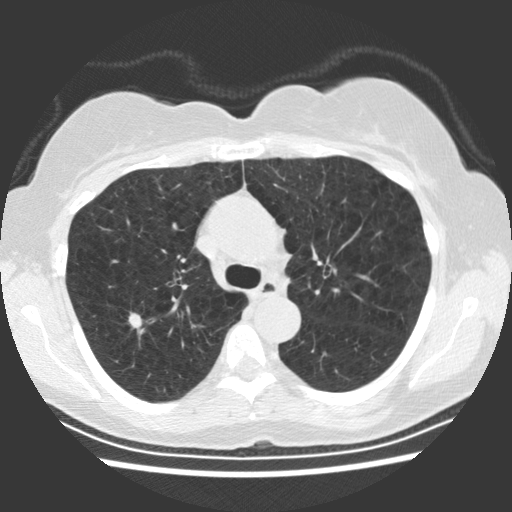
Chest CT (low-dose screening protocol), one axial image; baseline annual screen; lung window (W 1500 / L -600 HU); 2.5 mm slice thickness. Female, age 66 years at enrolment.
• Expert reader's lesion annotation, bounding box (x1, y1, x2, y2) in pixels: (111, 301, 153, 339).
• Screening reader's record for this exam (one nodule recorded; not confirmed to be the boxed lesion): non-calcified nodule or mass ≥4 mm, right upper lobe, 10 × 8 mm, smooth margins, soft tissue attenuation.
• Official screen result: positive, change unspecified: nodule(s) >= 4 mm or enlarging nodule(s), mass(es), or other non-specific abnormalities suspicious for lung cancer.